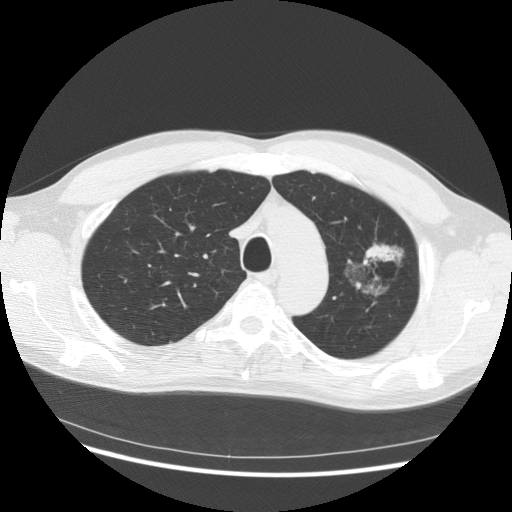
Low-dose screening chest CT, one axial slice; position 108 of 145 along the scan axis; reconstruction kernel STANDARD; 140 kVp; lung window (W 1500 / L -600 HU); 2.5 mm slice thickness; 512 × 512 image matrix, field of view 370 × 370 mm.
Outlined on this slice (manually delineated by an expert):
- lesion 1 (tumor, upper lobe of left lung): bounding box [x1, y1, x2, y2] px = [366, 245, 398, 261]